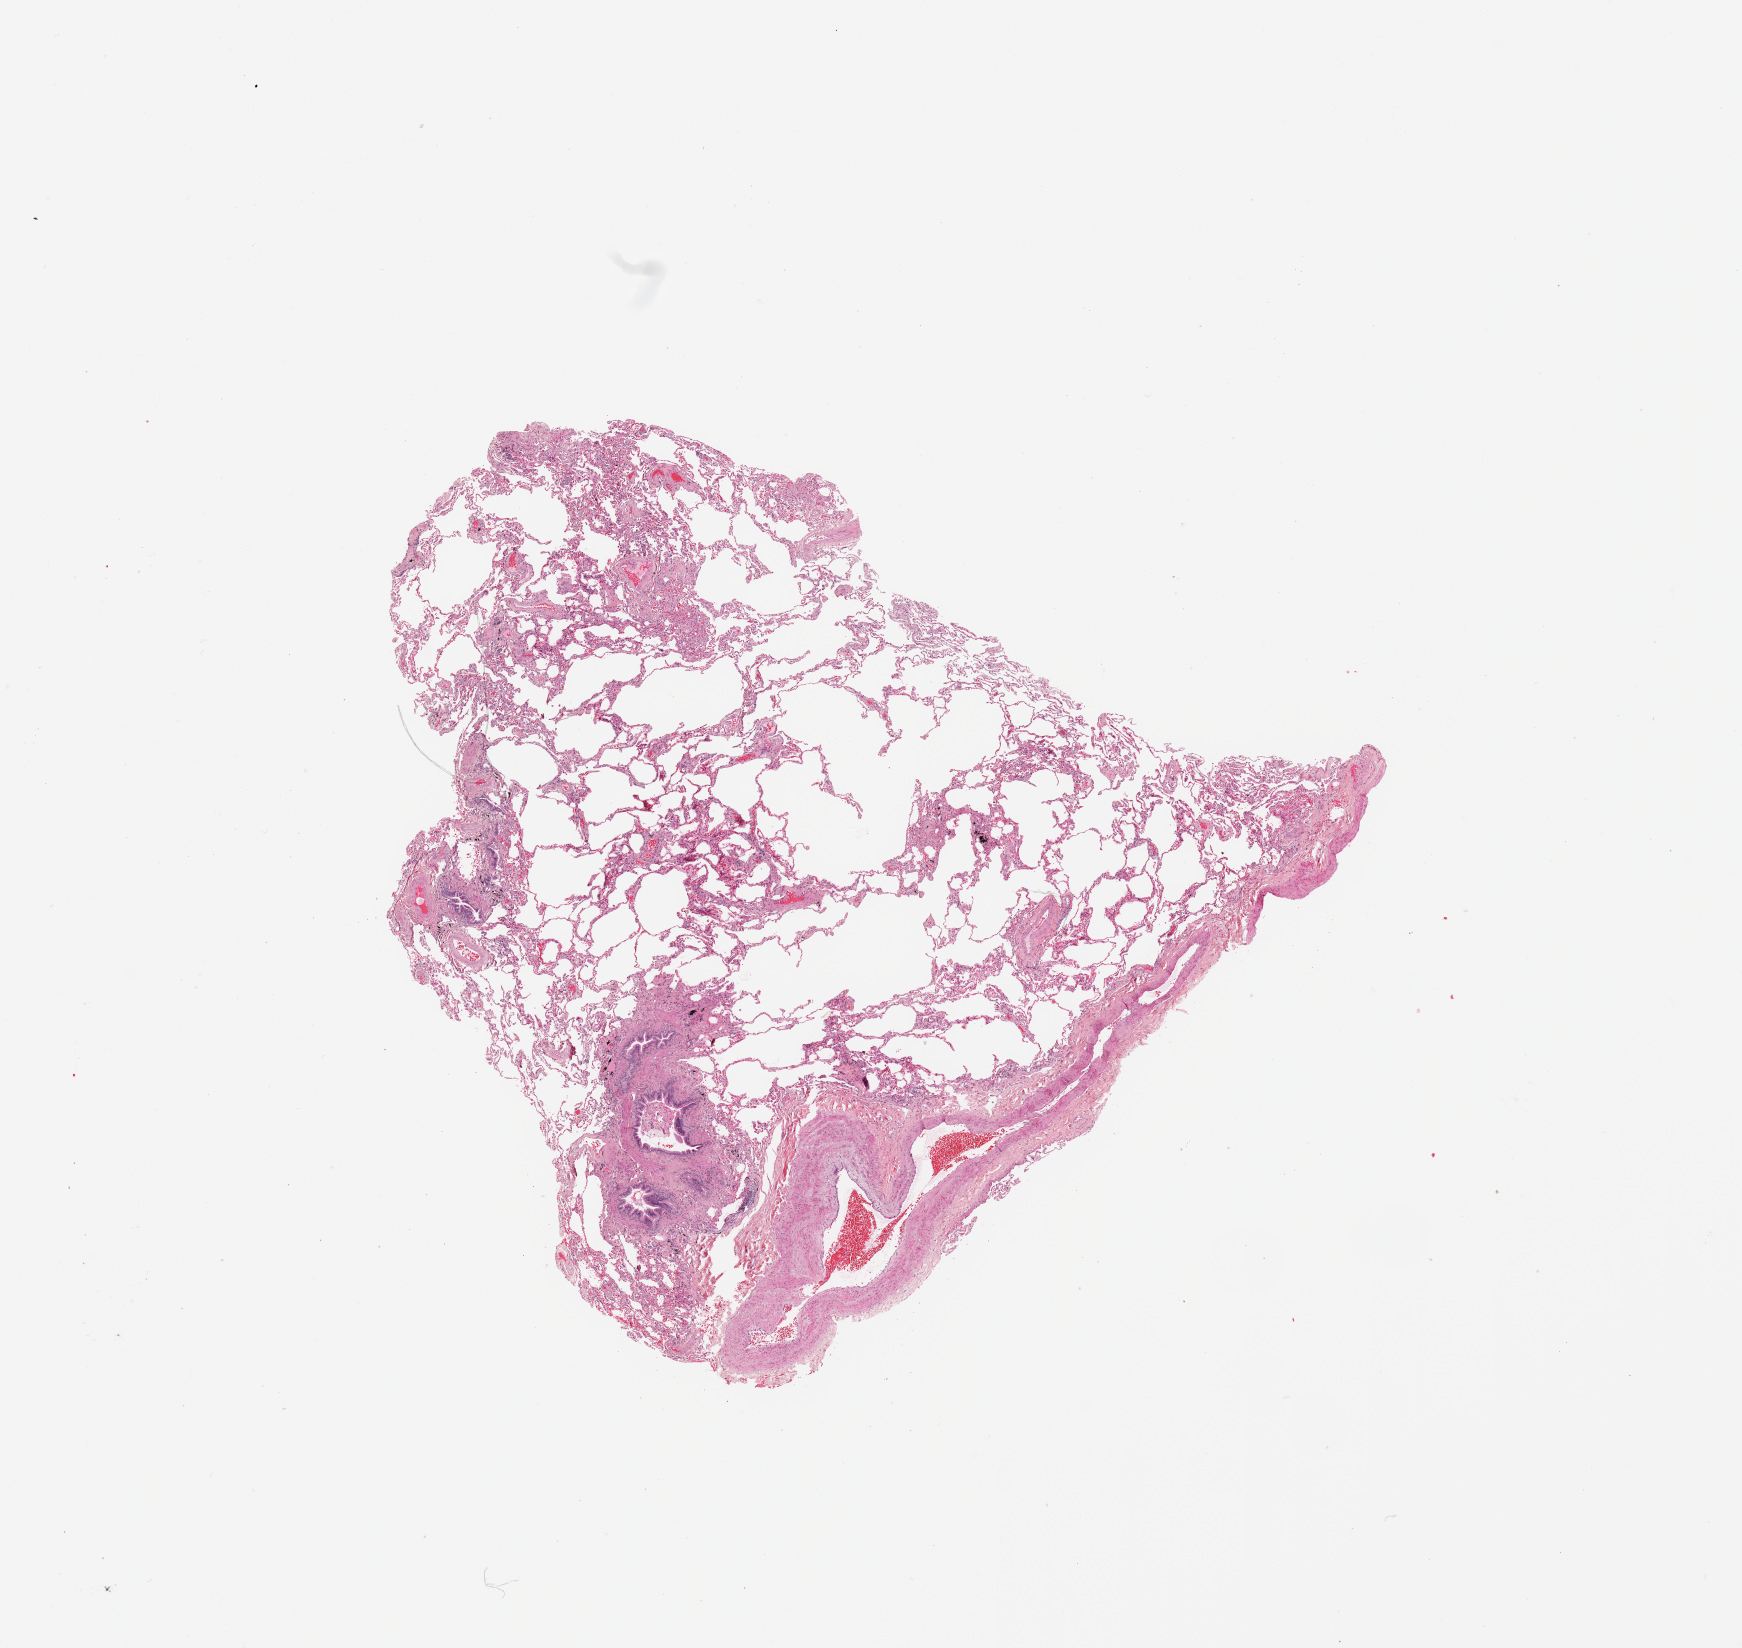
Whole-slide histology image, Hematoxylin and eosin (H&E) stained, low-resolution overview of the scanned area, about 13.8 x 13.0 mm (slide scanned at 20x), normal (non-tumour) tissue sample, sampled site: lung. Male, 78 y/o.
This section: normal (non-tumour) tissue from the same patient. Patient diagnosis: Squamous cell carcinoma, NOS.